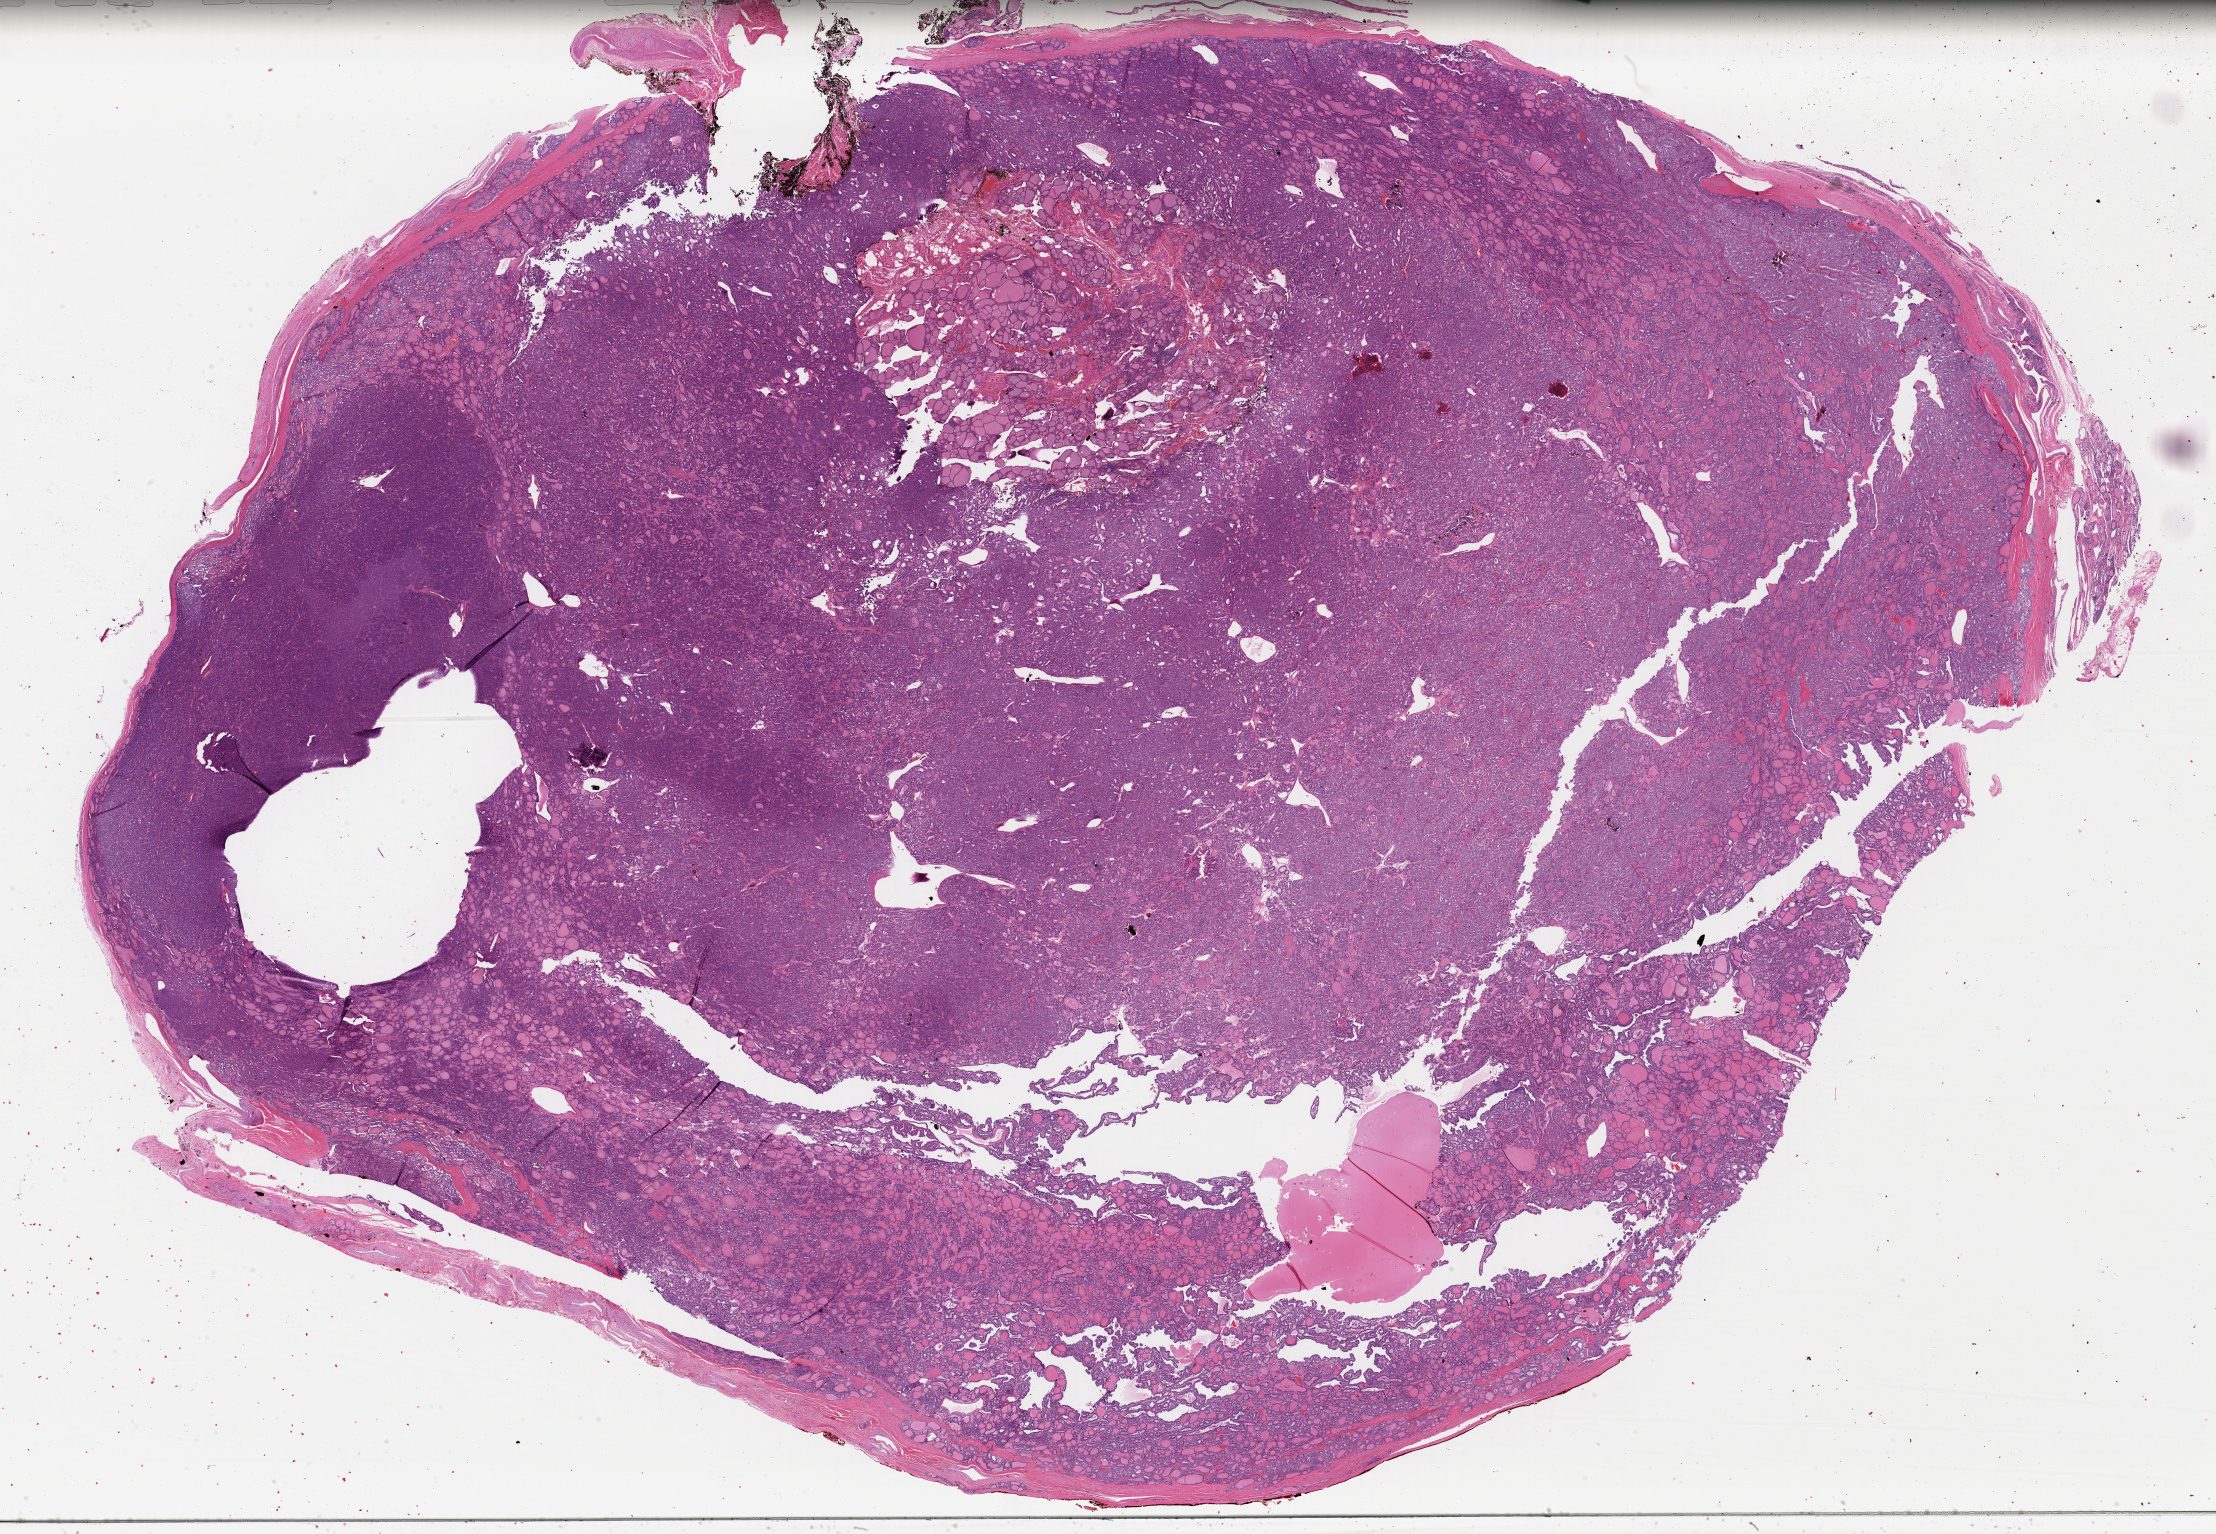
H&E whole-slide image — shown as a low-resolution overview of the whole scanned area (about 34.8 x 24.1 mm, acquisition: 40x scan), formalin-fixed paraffin-embedded (FFPE) diagnostic section, sample: primary tumour, thyroid. Female, age 53 years at initial diagnosis.
AJCC pathologic stage: III. Pathologic diagnosis: Papillary carcinoma, follicular variant (thyroid gland). Laterality: right.